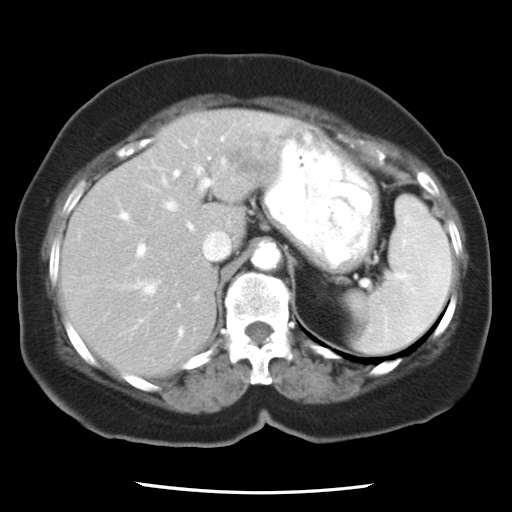
Contrast-enhanced abdominal CT, one axial slice. Slice 16 of 24 in the series (ordered by position). Intravenous contrast given. Soft-tissue window (W 400 / L 40 HU). 7.5 mm slice thickness. 512 × 512 image matrix, field of view 312 × 312 mm. Female patient, age 71 years. From the clinical record (not read from this slice): diagnosis: colorectal cancer liver metastases, imaged before liver resection; multiple liver metastases: no; largest metastasis: 4.3 cm.
Outlined on this slice (expert manual segmentation):
- hepatic veins: bounding box <121,177,231,367> (left, top, right, bottom; pixels)
- liver: <61,110,301,377>
- planned liver remnant (the part of the liver to remain after resection): <61,123,245,377>
- portal vein (with intrahepatic branches): <120,137,224,335>
- liver metastasis: <217,125,281,187>